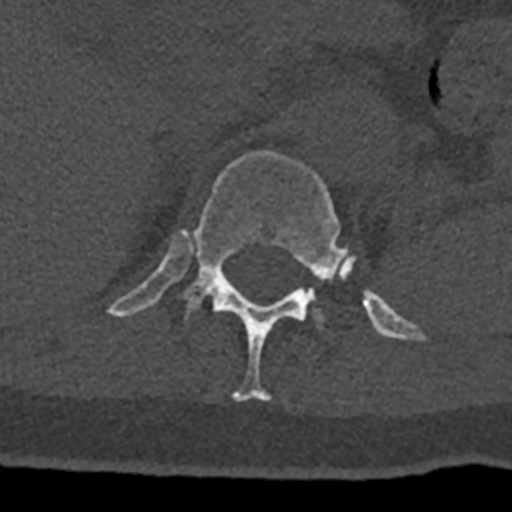
CT including the spine, one axial slice; slice 491 of 797 in the series (ordered by position); reconstruction kernel Br40s/3; 120 kVp; bone window (W 1800 / L 400 HU); 512 × 512 image matrix, field of view 160 × 160 mm. Male patient, age 74 years. Case-level facts recorded for this patient, not image findings: primary cancer: renal.
Annotated regions visible in this slice (semi-automatic segmentation, software-assisted and operator-edited):
- L1 vertebra: box from (x=309, y=298) to (x=324, y=326) px
- T12 vertebra: (x=107, y=150)–(x=426, y=402)